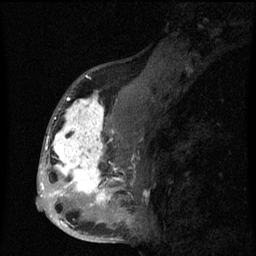
Breast MRI (dynamic contrast-enhanced), one sagittal slice. Dynamic contrast-enhanced series, image 2 of 3 at this slice position (ordered by acquisition). 1.5 T. TE 4.2 ms, TR 8 ms. 2 mm slice thickness. 256 × 256 image matrix, field of view 190 × 190 mm. Female patient, age 50 years.
Outlined on this slice (semi-automatic segmentation, software-assisted and operator-edited):
- analysis volume of interest (the breast-tissue region the enhancement analysis was run in; not a lesion): bounding box <43,90,142,216> (left, top, right, bottom; pixels)
- tumour enhancement mask (voxels above the 70 % enhancement threshold inside the analysis volume of interest): <43,91,123,206>